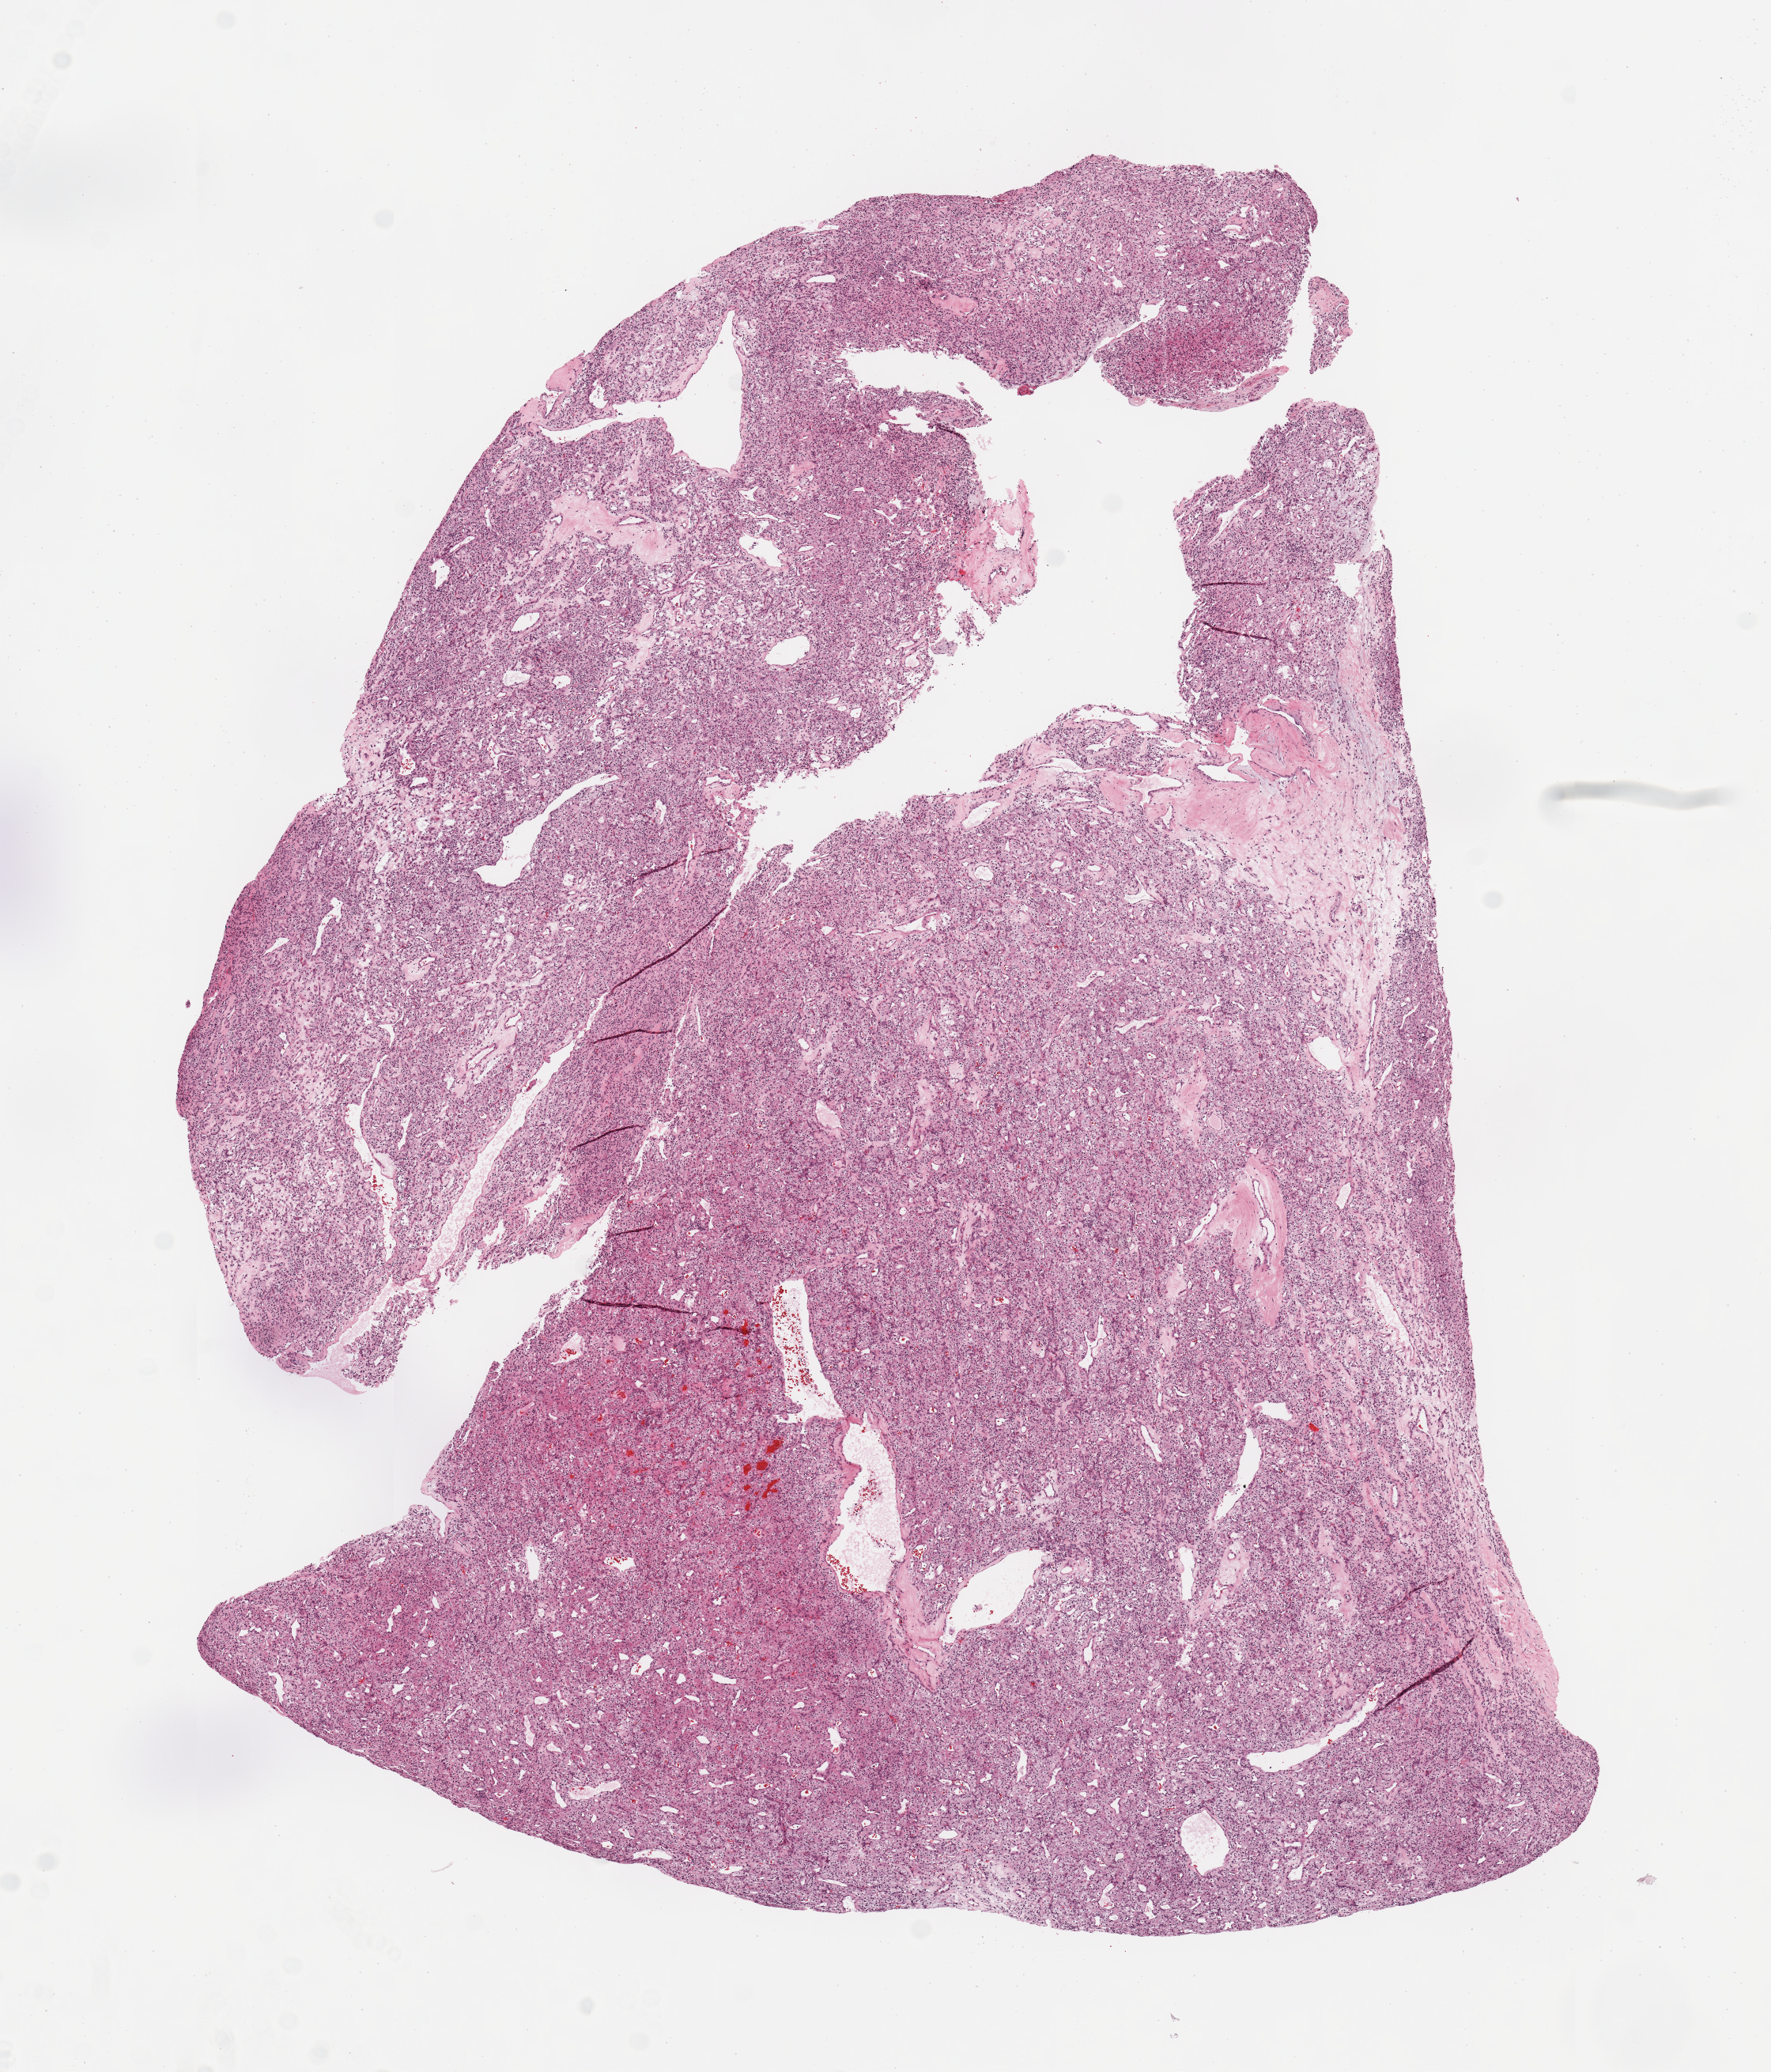
H&E-stained whole-slide image, a low-resolution overview of the entire scanned area, about 8.9 x 10.4 mm. Tumour tissue sample, sampled site: kidney. Patient: female, age 75 years. Histologic grade: G3 (poorly differentiated). Pathologist review of this section (percent, as recorded): tumour nuclei 90%, necrosis 2%.
Histologic diagnosis: Renal cell carcinoma, NOS. AJCC pathologic stage: III.